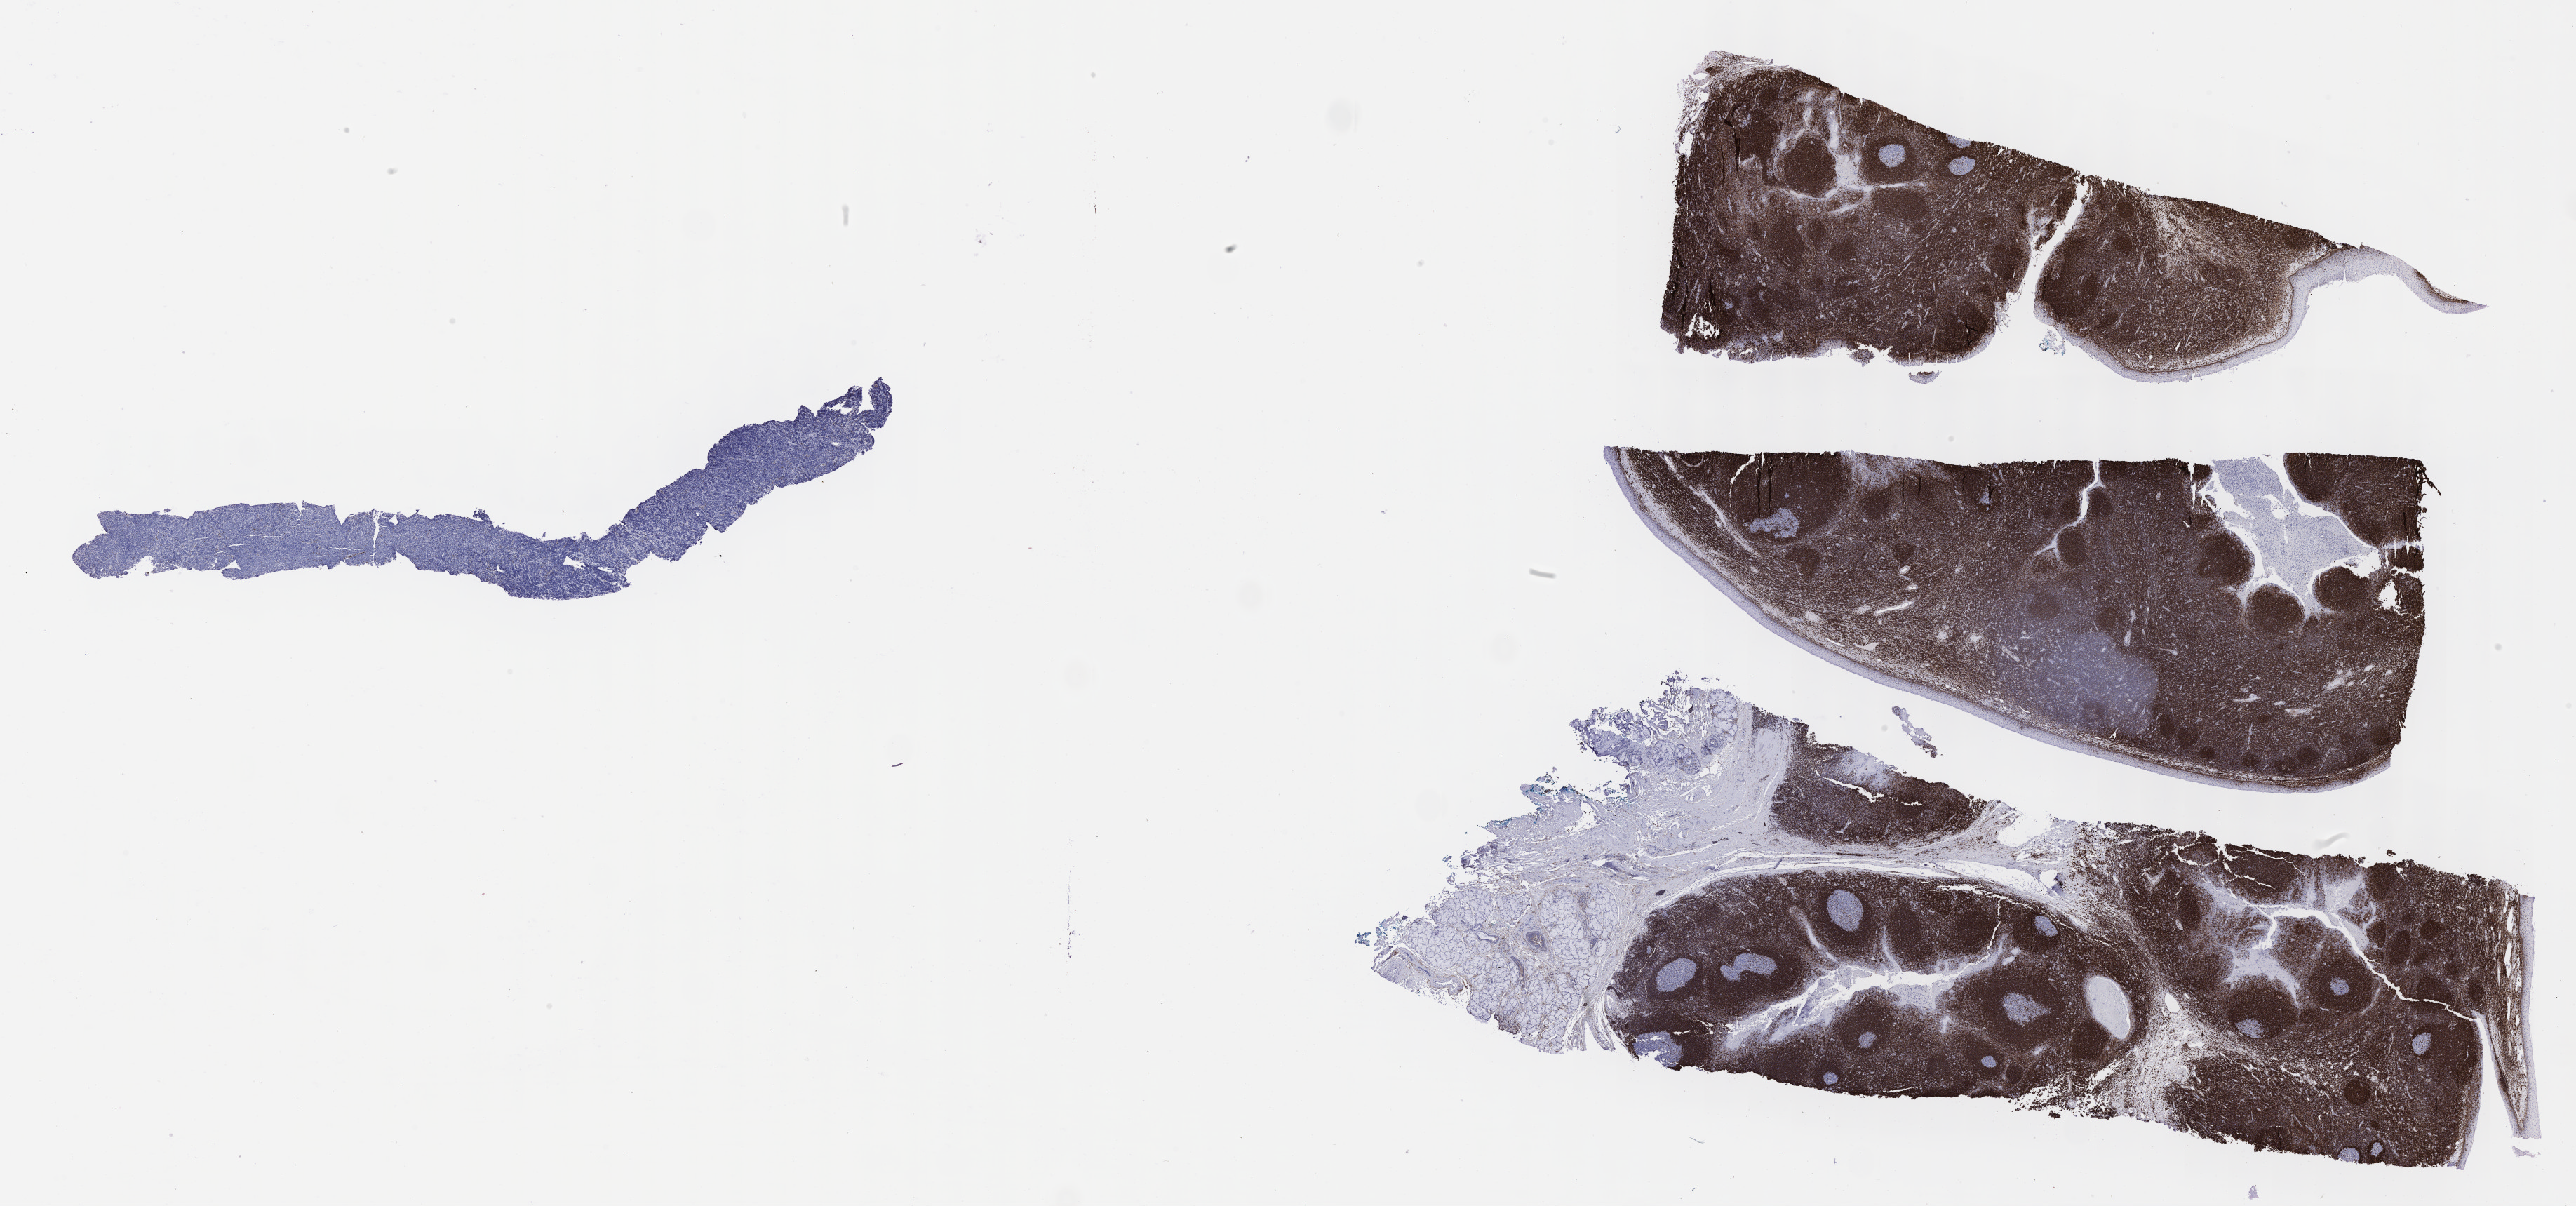
IHC for BCL2, whole-slide image, low-resolution overview of the scanned area, about 29.7 x 13.9 mm. Specimen: tumor tissue. Anatomic site: kidney. Male, age 9 years at initial diagnosis.
Histologic diagnosis: Burkitt lymphoma, NOS.